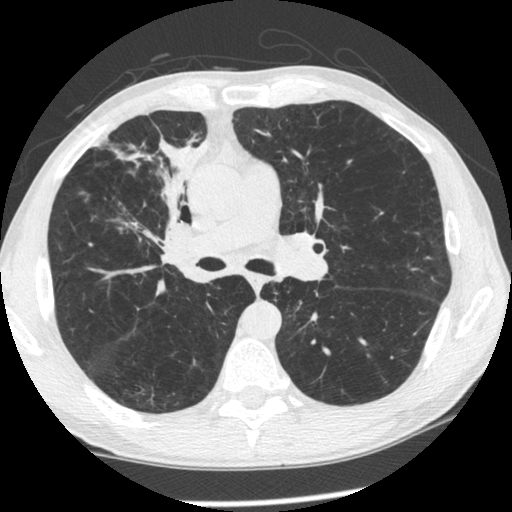
Low-dose screening chest CT, one axial slice. Slice 139 of 261 in the series (ordered by position). Reconstruction kernel STANDARD. Lung window (W 1500 / L -600 HU). 1.25 mm slice thickness. 512 × 512 image matrix, field of view 340 × 340 mm.
Outlined on this slice (expert manual segmentation):
- lesion 1 (tumor, upper lobe of right lung): bounding box [x1, y1, x2, y2] px = [115, 139, 209, 236]